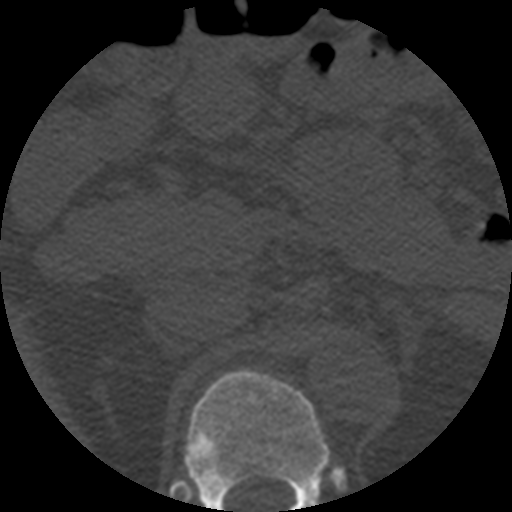
CT including the spine, one axial slice; slice 220 of 508 in the series (ordered by position); reconstruction kernel STANDARD; bone window (W 1800 / L 400 HU); 1.25 mm slice thickness; 512 × 512 image matrix, field of view 160 × 160 mm. Patient age 57 years. Case-level facts recorded for this patient, not image findings: primary cancer: prostate.
Annotated regions visible in this slice (semi-automatically segmented with operator editing):
- T12 vertebra: bounding box [x1, y1, x2, y2] px = [184, 370, 331, 512]